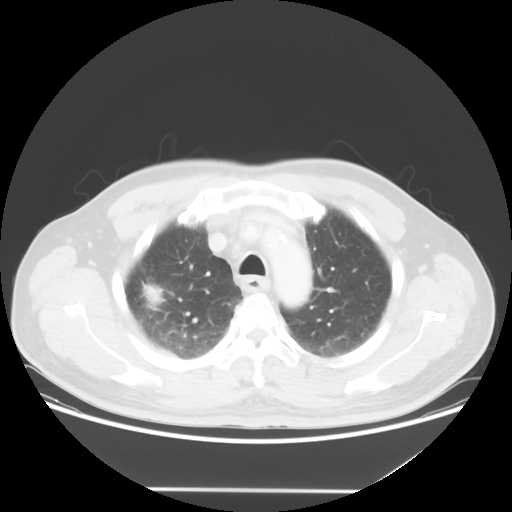
Chest CT, one axial slice; slice 42 of 54 in the series (ordered by position); reconstruction kernel STANDARD; 120 kVp; lung window (W 1500 / L -600 HU); 5 mm slice thickness; 512 × 512 image matrix, field of view 416 × 416 mm. Patient: male, 65 years. From the clinical record (not read from this slice): clinical TNM (as recorded): T1c N1 M0.
Structures marked on this image (bounding box drawn by a radiologist):
- lung tumour (recorded histology: adenocarcinoma): bounding box [x1, y1, x2, y2] px = [139, 270, 166, 318]